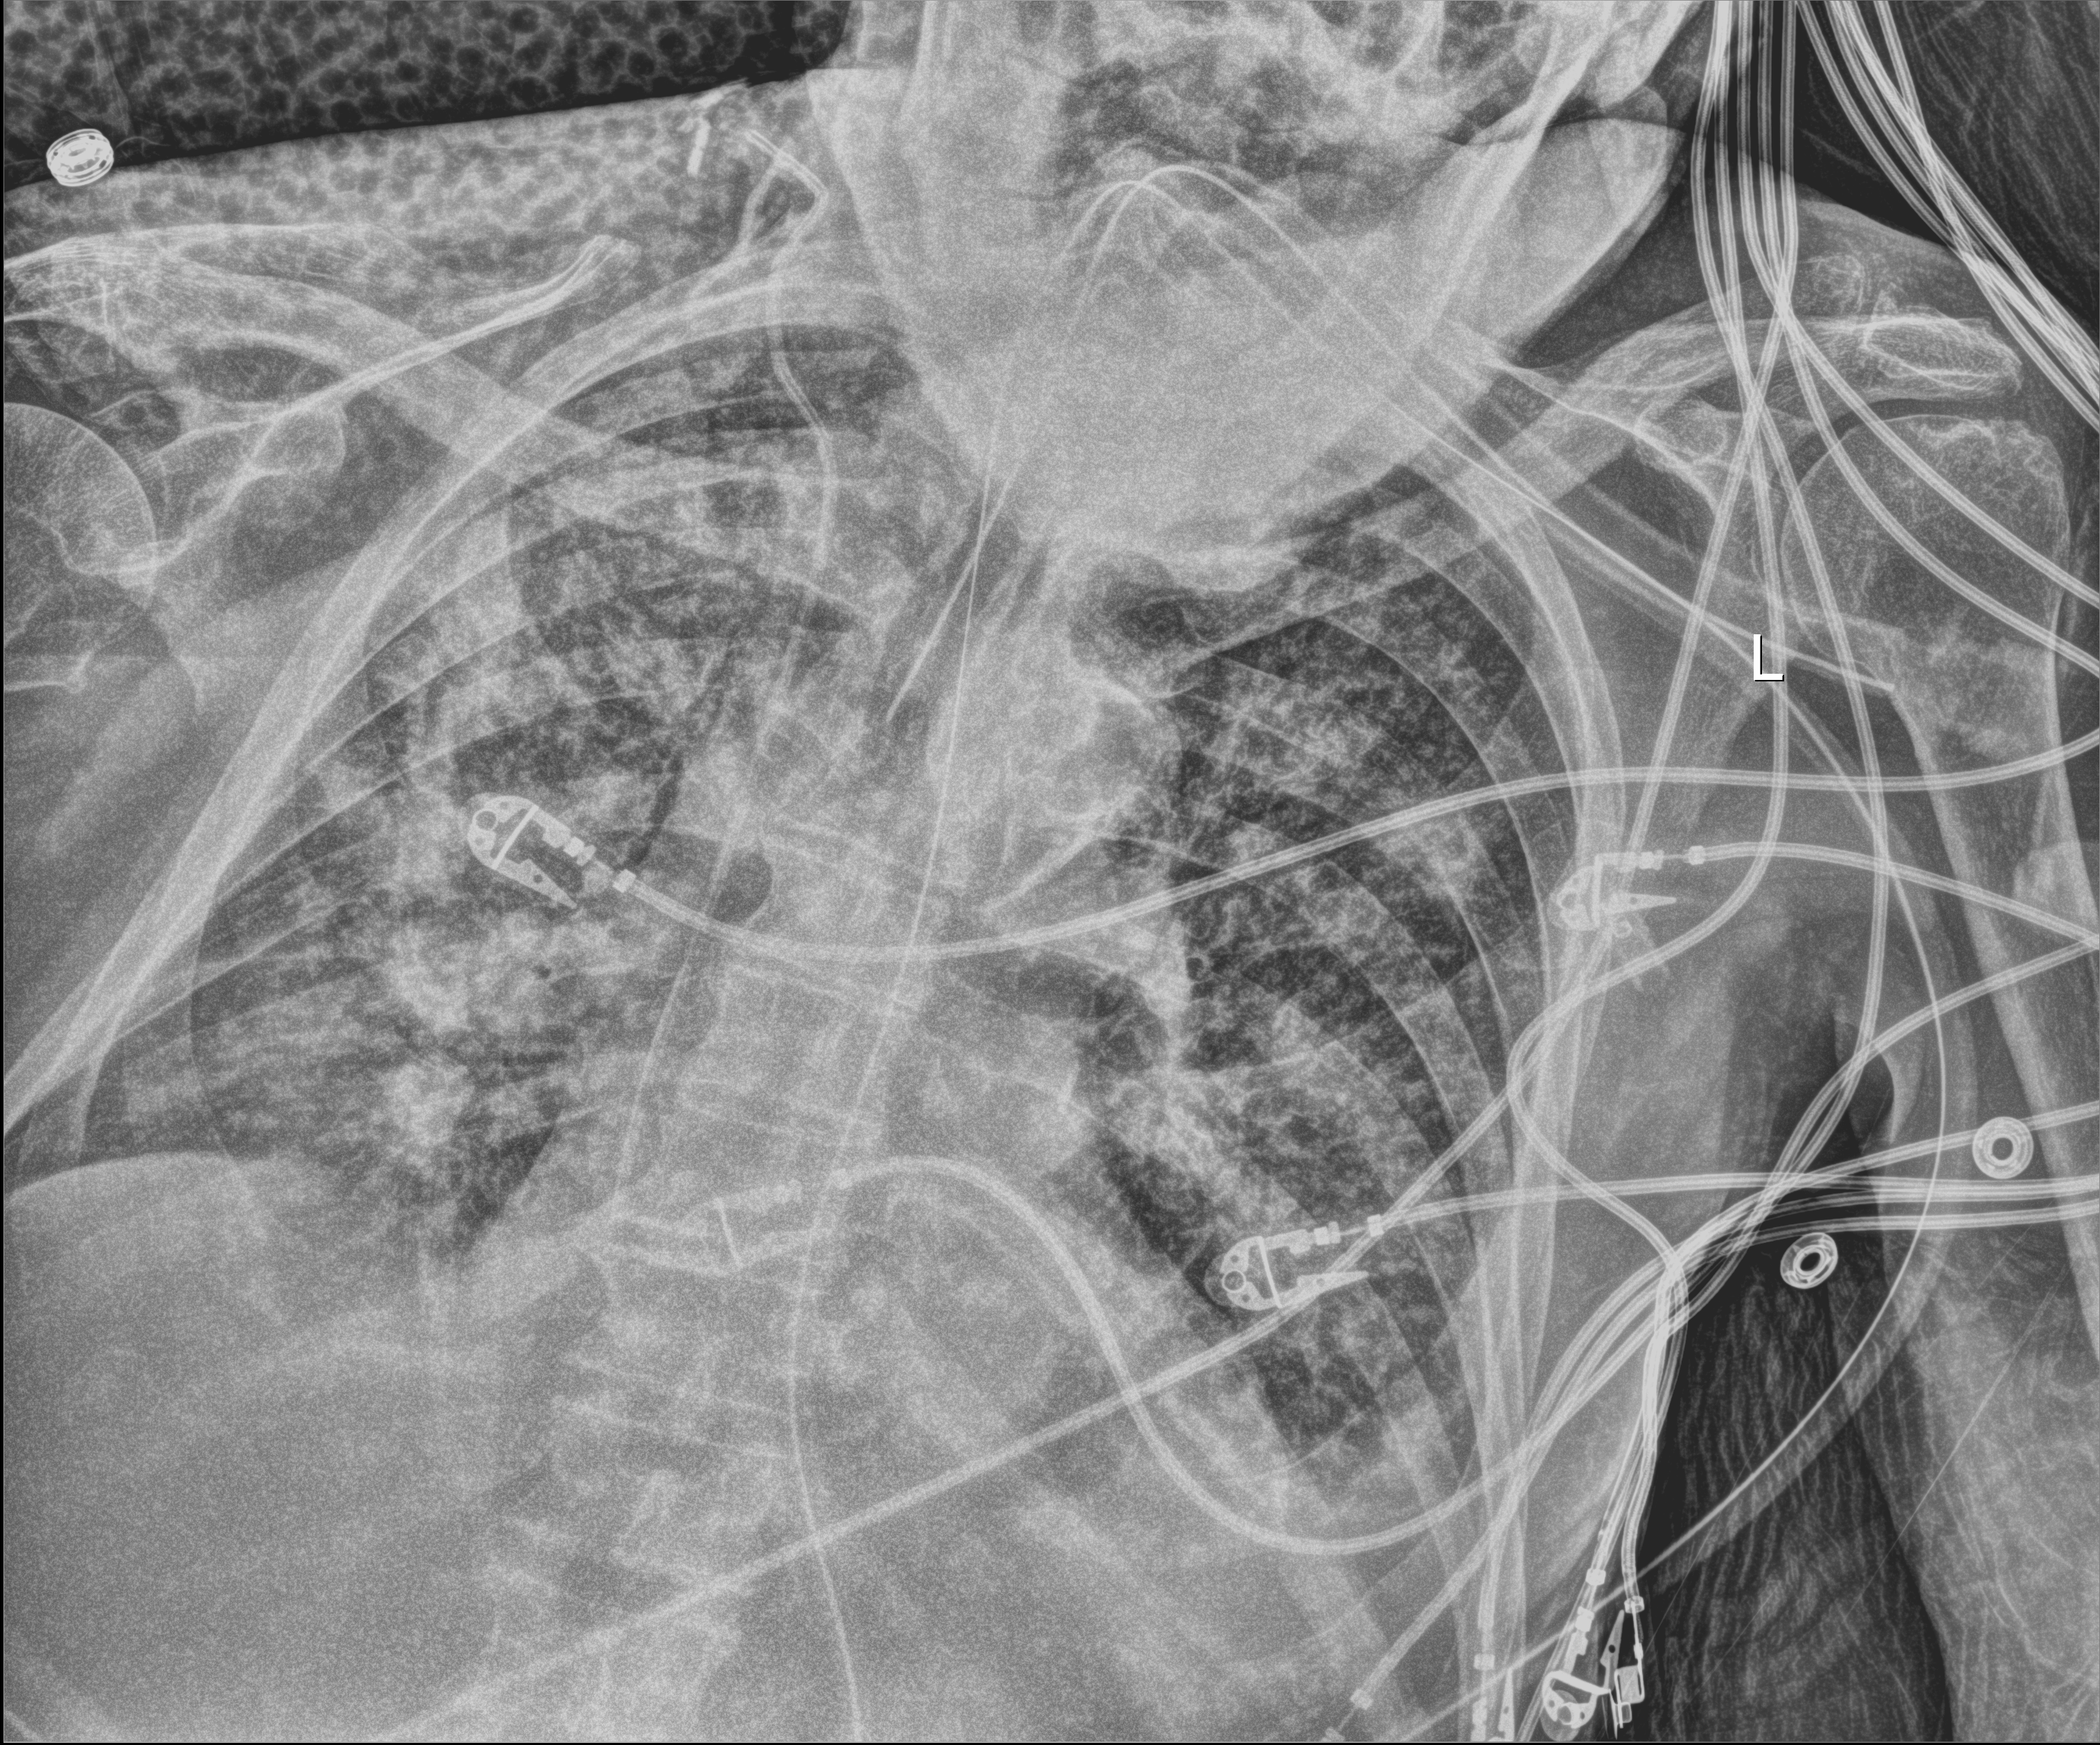
Bedside chest radiograph (digital radiography). Patient hospitalised with COVID-19; male, aged 75–90 years.
Admission-level facts for this patient (not findings on this image; timing relative to this image not recorded): chronic kidney disease (admission record): no; mechanically ventilated during this hospital stay: yes; admitted to intensive care during this hospital stay: yes.